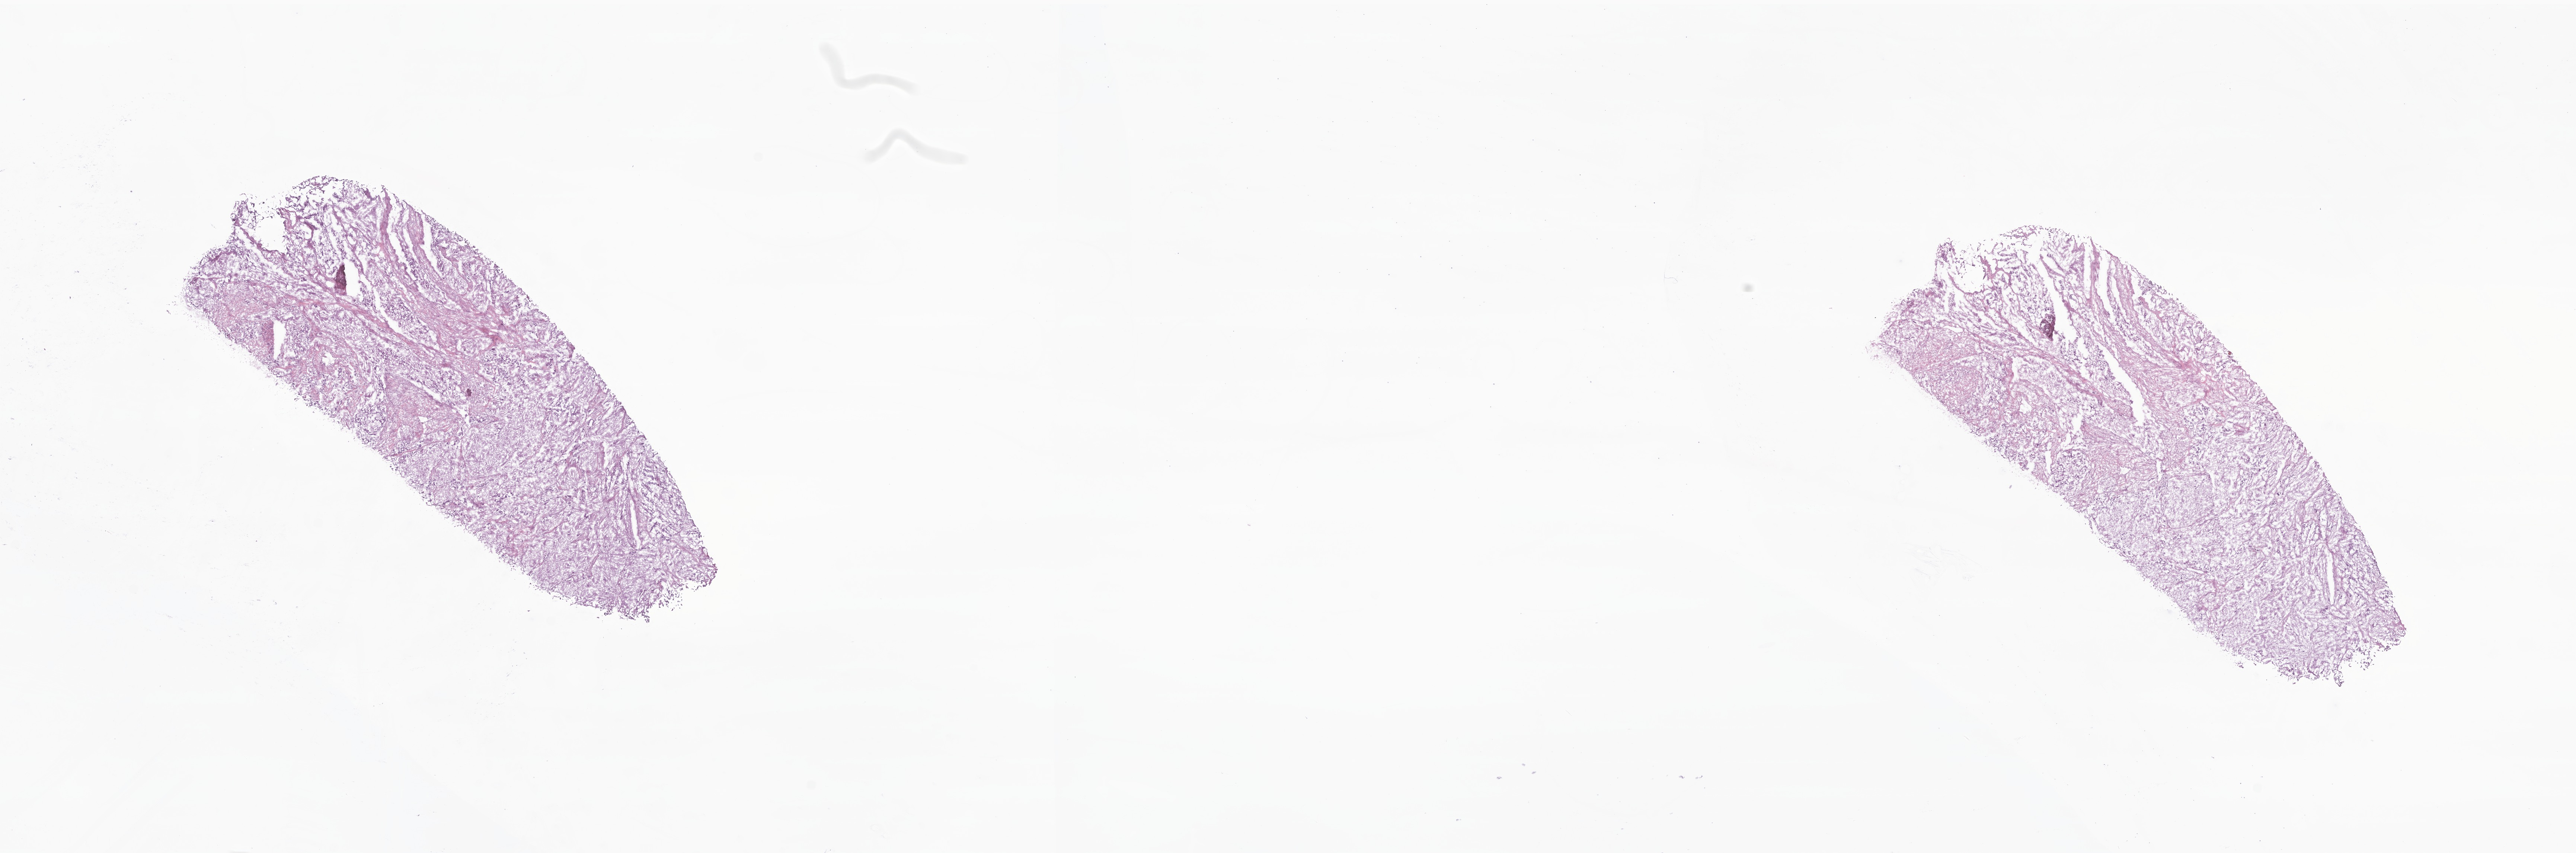
Digitized haematoxylin and eosin-stained section of tumor tissue from the abdomen, shown as a low-resolution overview of the whole scanned area (about 29.2 x 9.7 mm). Cryosection (OCT / tissue freezing medium). Patient: male, age 49 months (4 years 1 month).
Diagnosis (ICD-O-3 morphology term): Neuroblastoma, NOS.